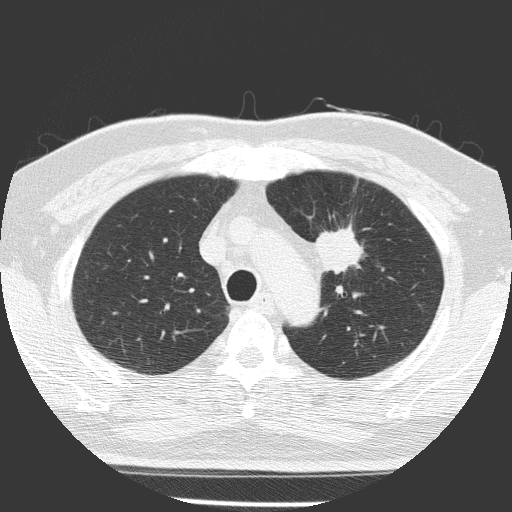
Chest CT (low-dose screening protocol), one axial image; first (baseline) screen; lung window (W 1500 / L -600 HU); slice 41 of 156 in the series. Male participant, aged 70 years at enrolment. Current smoker at enrolment.
Lesion marked by an expert reader, bounding box (x1, y1, x2, y2) in pixels: (297, 221, 372, 295). The screening reader recorded 3 non-calcified nodules or masses ≥4 mm on this exam (left upper lobe, left lower lobe, left upper lobe); which of them this box marks is not recorded. Lung cancer was diagnosed 58 days after this screen: squamous cell carcinoma, NOS, left upper lobe, poorly differentiated (G3), stage IB (AJCC 6th edition), 47 mm at pathology.